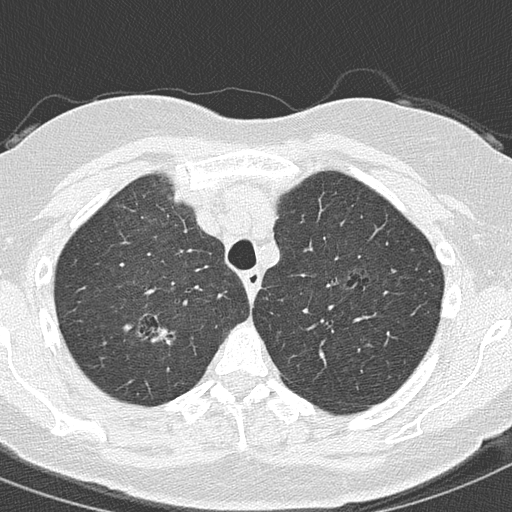
Axial slice from a low-dose chest CT screening exam. Second screening round (one year after baseline). Lung window (W 1500 / L -600 HU). Slice 36 of 157 in the series. 512 × 512 image matrix, field of view 280 × 280 mm. Female participant, aged 61 years at enrolment. Current smoker at enrolment.
- Expert-annotated lung lesion, box from (x=142, y=312) to (x=185, y=353) px.
- The exam's reader record, not a measurement of the box and not confirmed to be the same lesion: non-calcified nodule or mass ≥4 mm, right upper lobe, 15 × 10 mm, spiculated (stellate) margins, ground glass attenuation, pre-existing on the prior screen: yes; interval growth: yes.
- Official screen result: positive, other.
- Later outcome: lung cancer diagnosed 91 days after this screen — adenocarcinoma, NOS, right upper lobe, moderately differentiated (G2), stage IA (AJCC 6th edition), 20 mm at pathology.